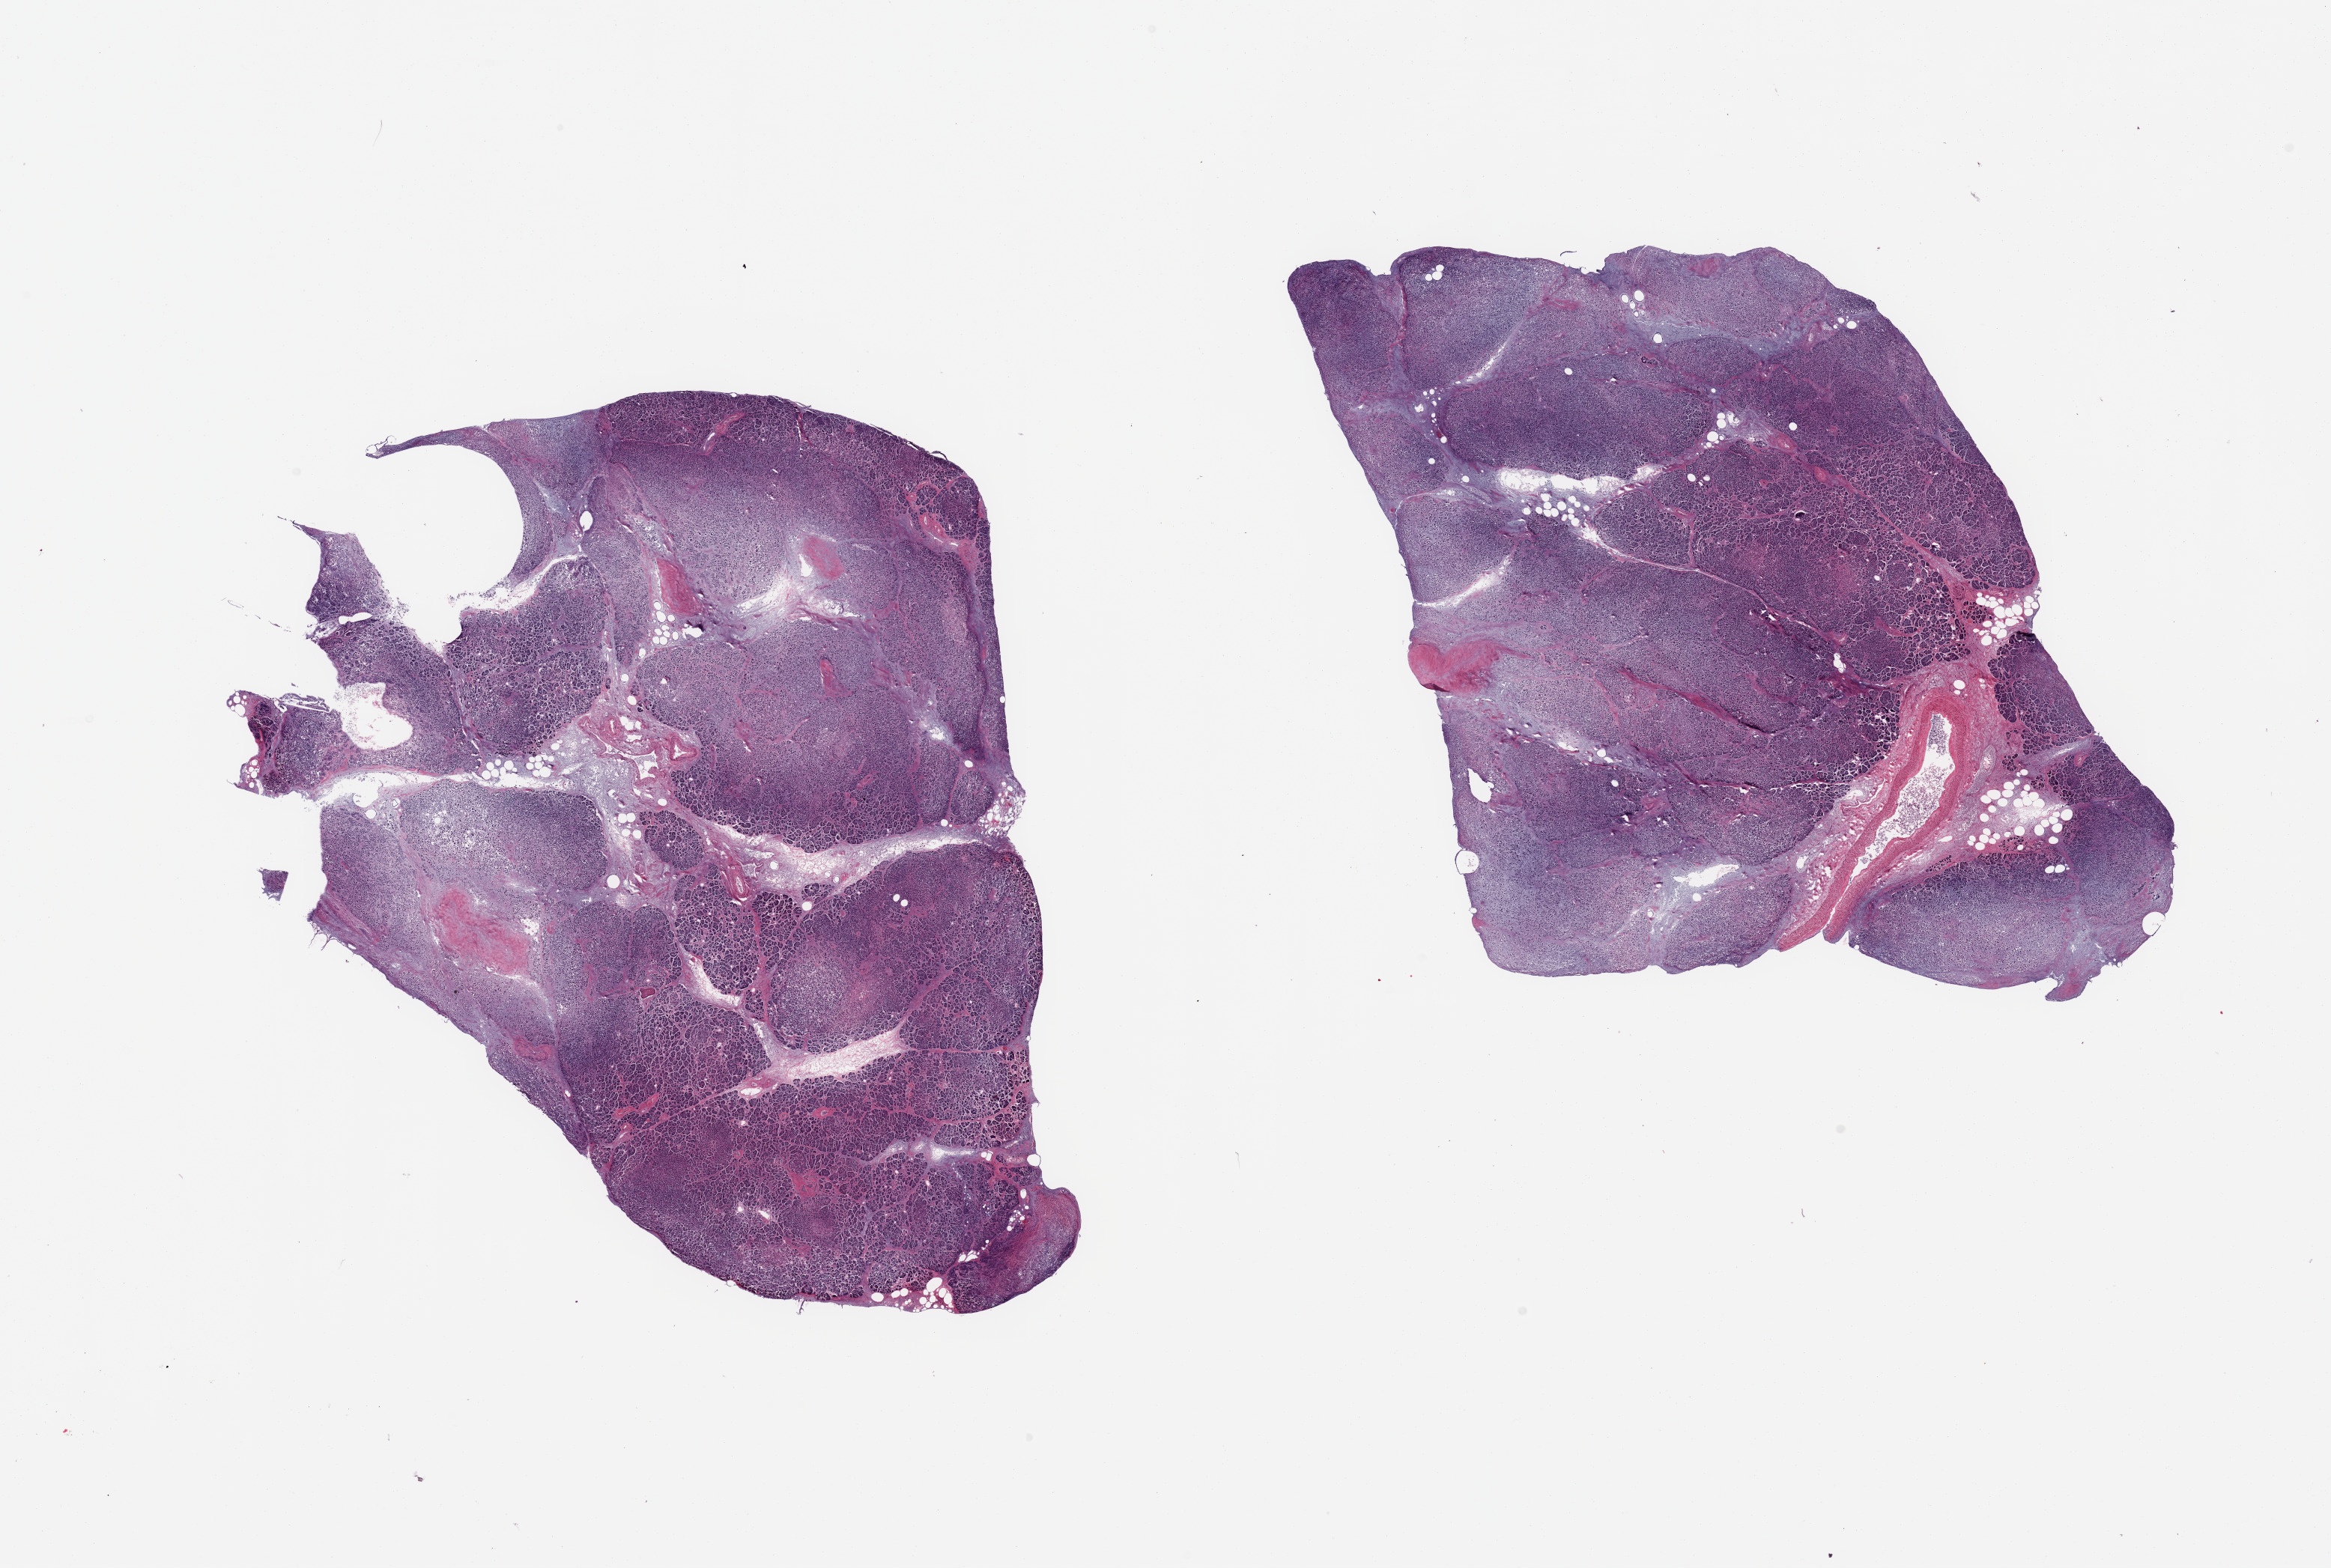
Whole-slide image, haematoxylin and eosin stain, brightfield, whole scanned area (about 24.6 x 16.6 mm) shown as a low-resolution overview. PAXgene-fixed, paraffin-embedded tissue. Section of pancreas (target tissue). Donor tissue sample. Donor sex: male.
Pathologist's review note for this sample: 2 pieces; severe autolysis involving internal fat, parenchyma and Langerhans islets.